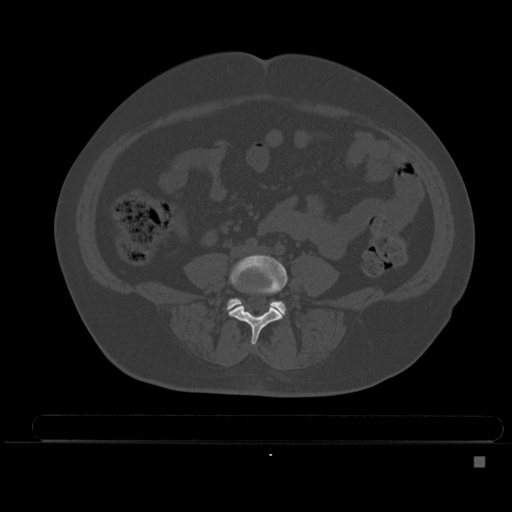
CT including the spine, one axial slice; bone window (W 1800 / L 400 HU); 512 × 512 image matrix, field of view 404 × 404 mm. Female patient, age 33 years. Case-level facts recorded for this patient, not image findings: primary cancer: breast; vertebrae with lytic lesions (as recorded): T1.
Annotated regions visible in this slice (semi-automatic segmentation, software-assisted and operator-edited):
- L4 vertebra: bounding box [x1, y1, x2, y2] px = [229, 254, 287, 345]
- L5 vertebra: [227, 298, 286, 316]